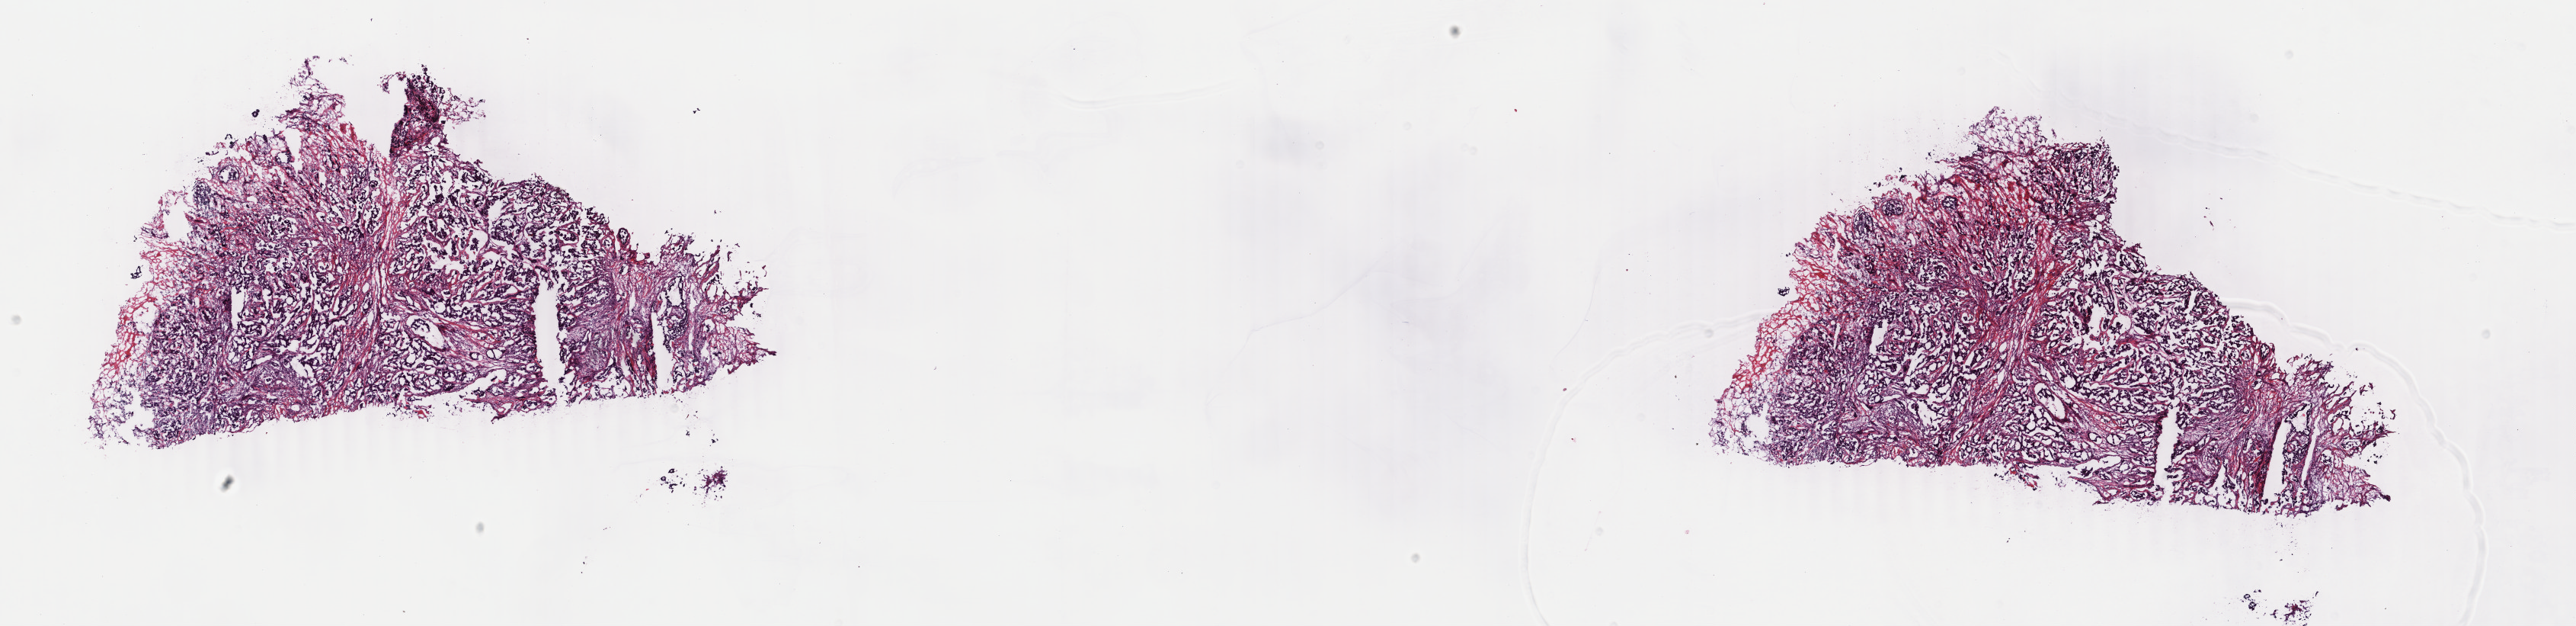
H&E-stained whole-slide image, whole scanned area (about 26.9 x 6.5 mm) shown as a low-resolution overview. Frozen section from the top of the tissue portion. Primary tumour sample from the breast. Female, age 49 years at initial diagnosis. Pathologist review of this section (percent, as recorded): tumour cells 85%, tumour nuclei 85%, normal cells 0%, stromal cells 15%, necrosis 0%. Infiltration values recorded for this section: lymphocyte infiltration 1%, monocyte infiltration 0%, neutrophil infiltration 0%.
TNM: T2 N1b M0. AJCC pathologic stage: IIB (3rd edition). Laterality: right. Histologic diagnosis: Infiltrating duct carcinoma, NOS. Lymph nodes positive (case pathology): 5 of 13 examined.